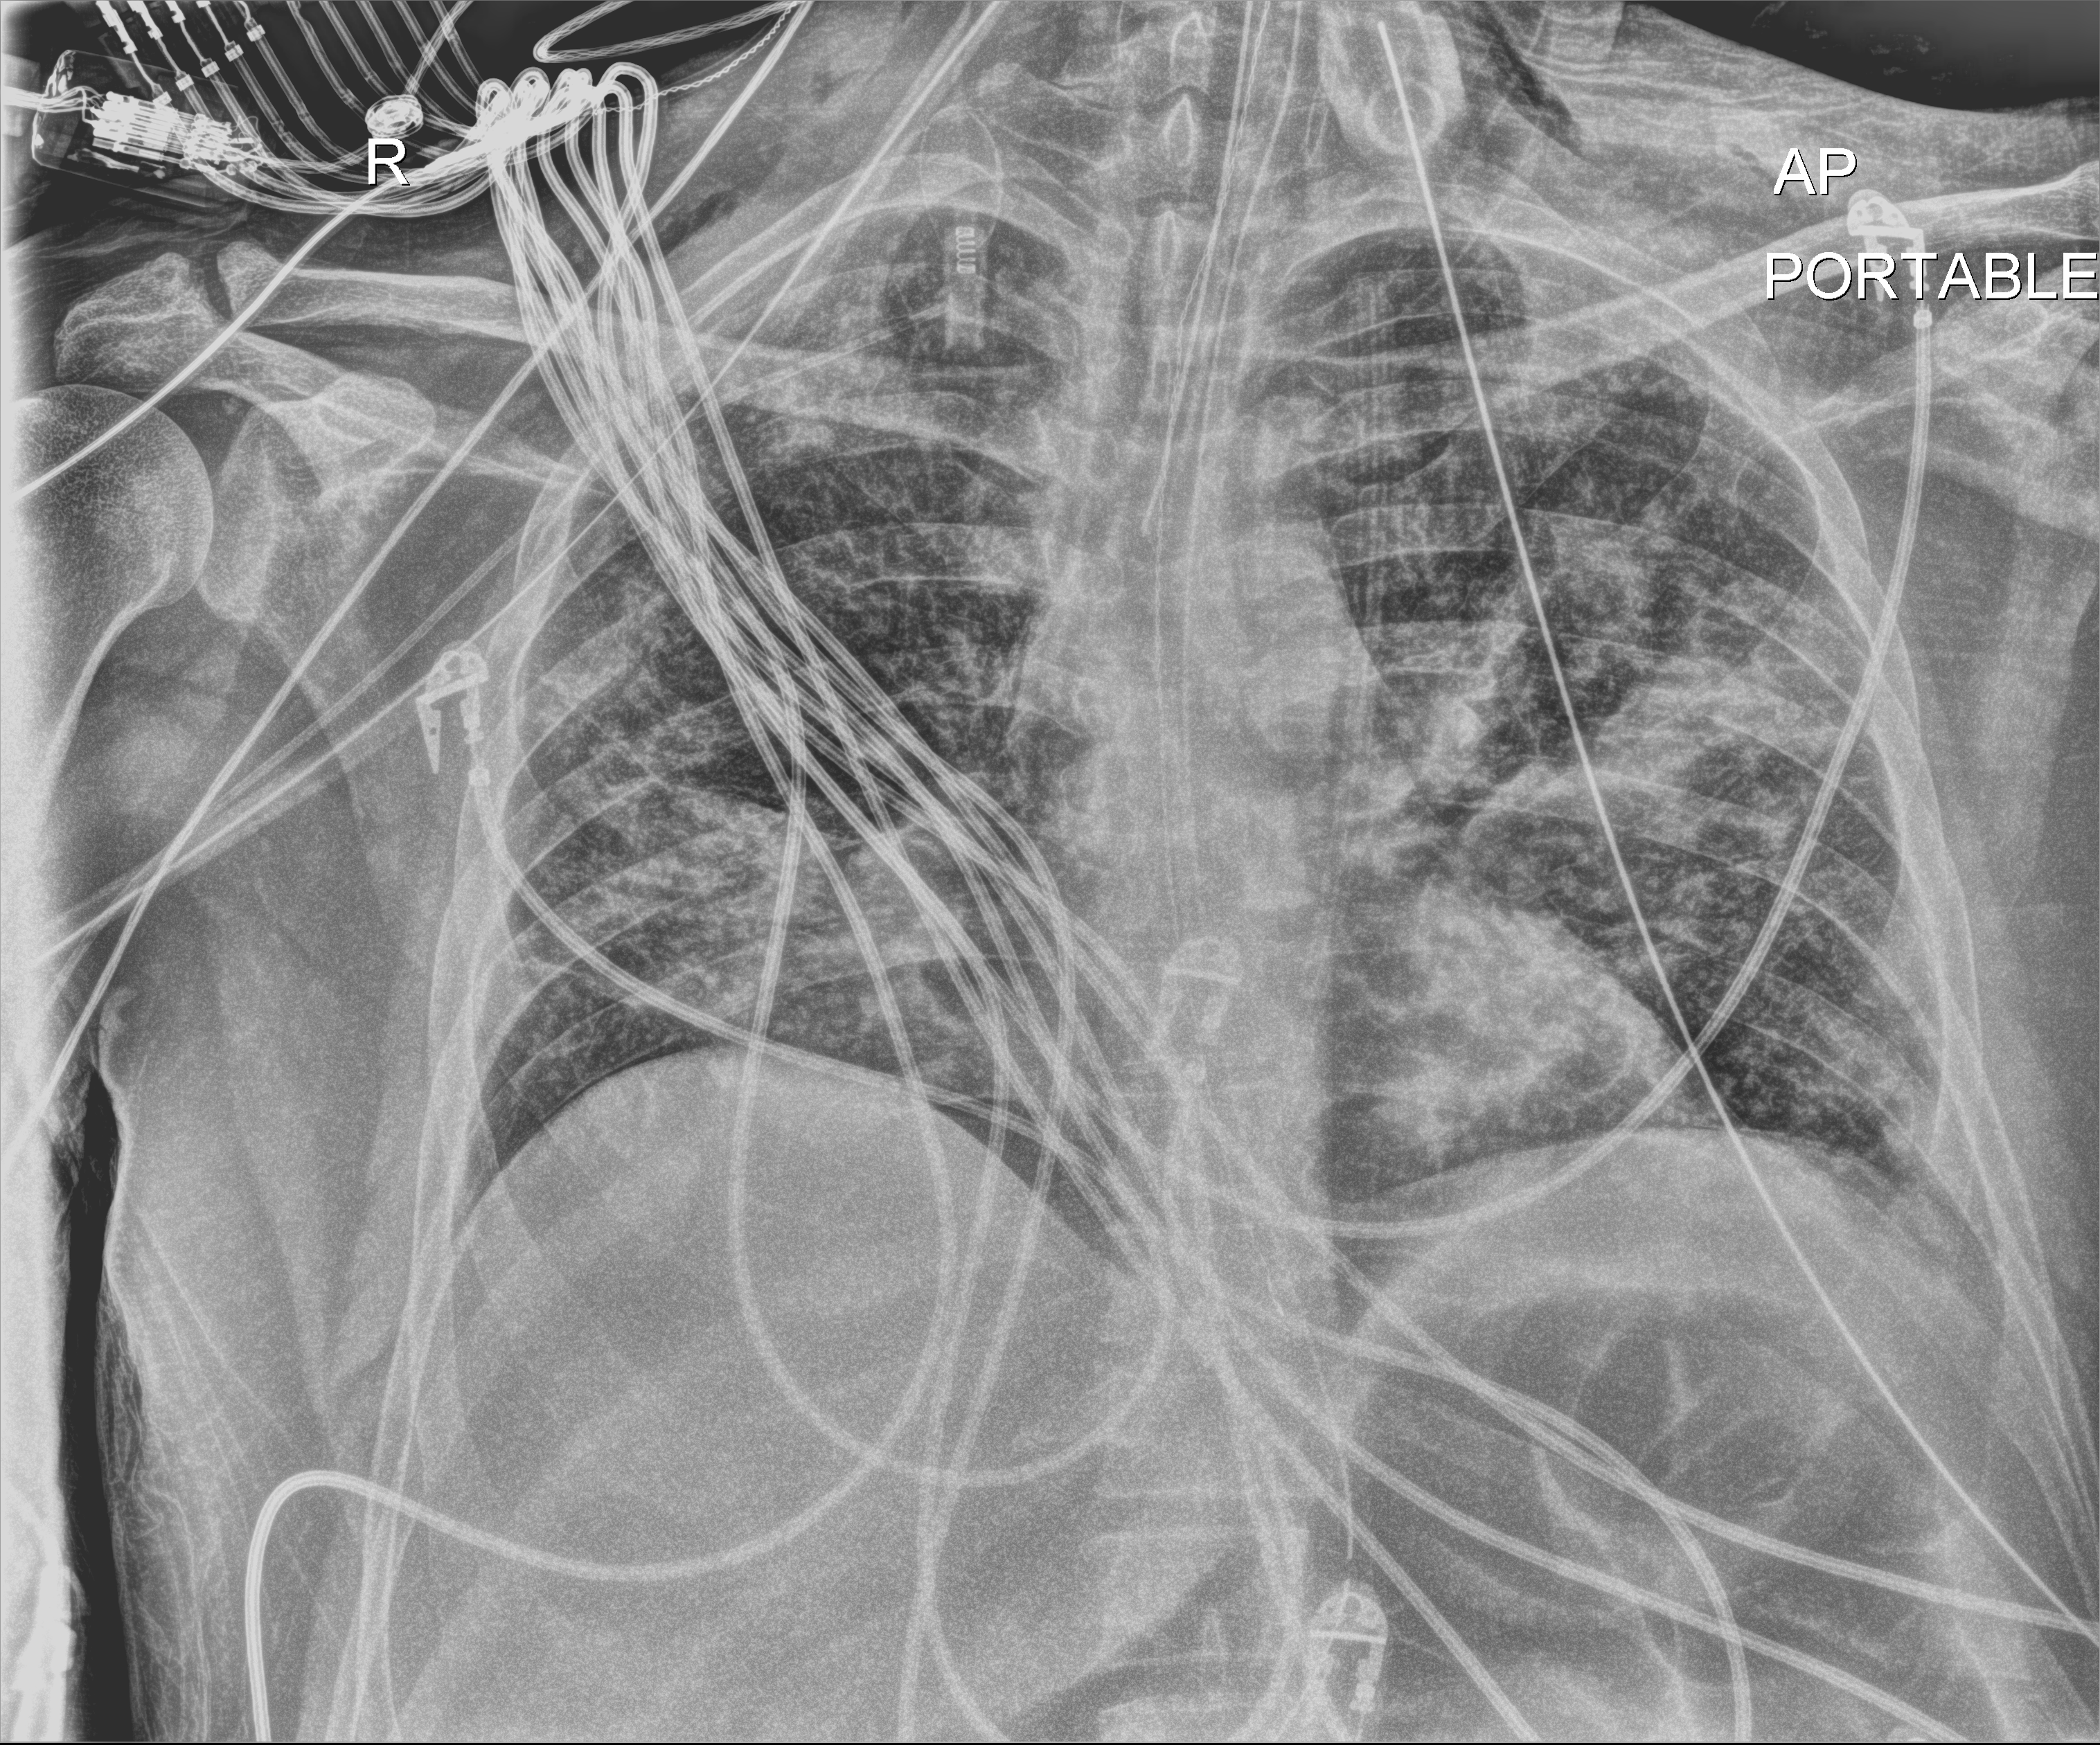
Chest radiograph; anteroposterior (AP) projection. Patient hospitalised with COVID-19, aged 18–59 years.
Admission-level facts for this patient (not findings on this image; timing relative to this image not recorded): mechanically ventilated during this hospital stay: yes; length of hospital stay: 50 days.